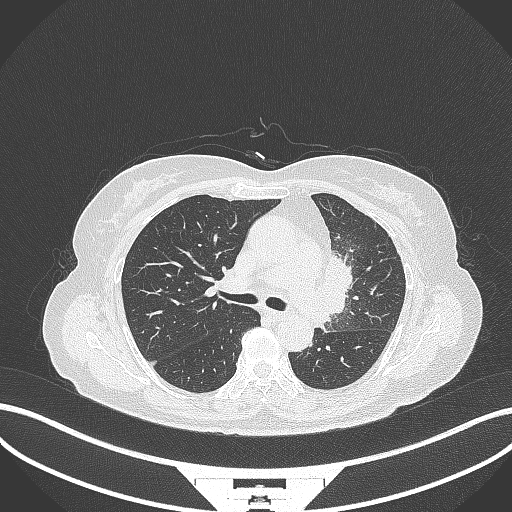
Chest CT, one axial slice. Position 210 of 382 along the scan axis. 120 kVp. Lung window (W 1500 / L -600 HU). 1 mm slice thickness. 512 × 512 image matrix. Female patient, age 64 years. Case-level facts recorded for this patient, not image findings: clinical TNM (as recorded): T2a N2 M0.
Outlined on this slice (rectangle marked by the reading radiologist):
- lung tumour (recorded histology: adenocarcinoma): box from (x=319, y=248) to (x=356, y=318) px